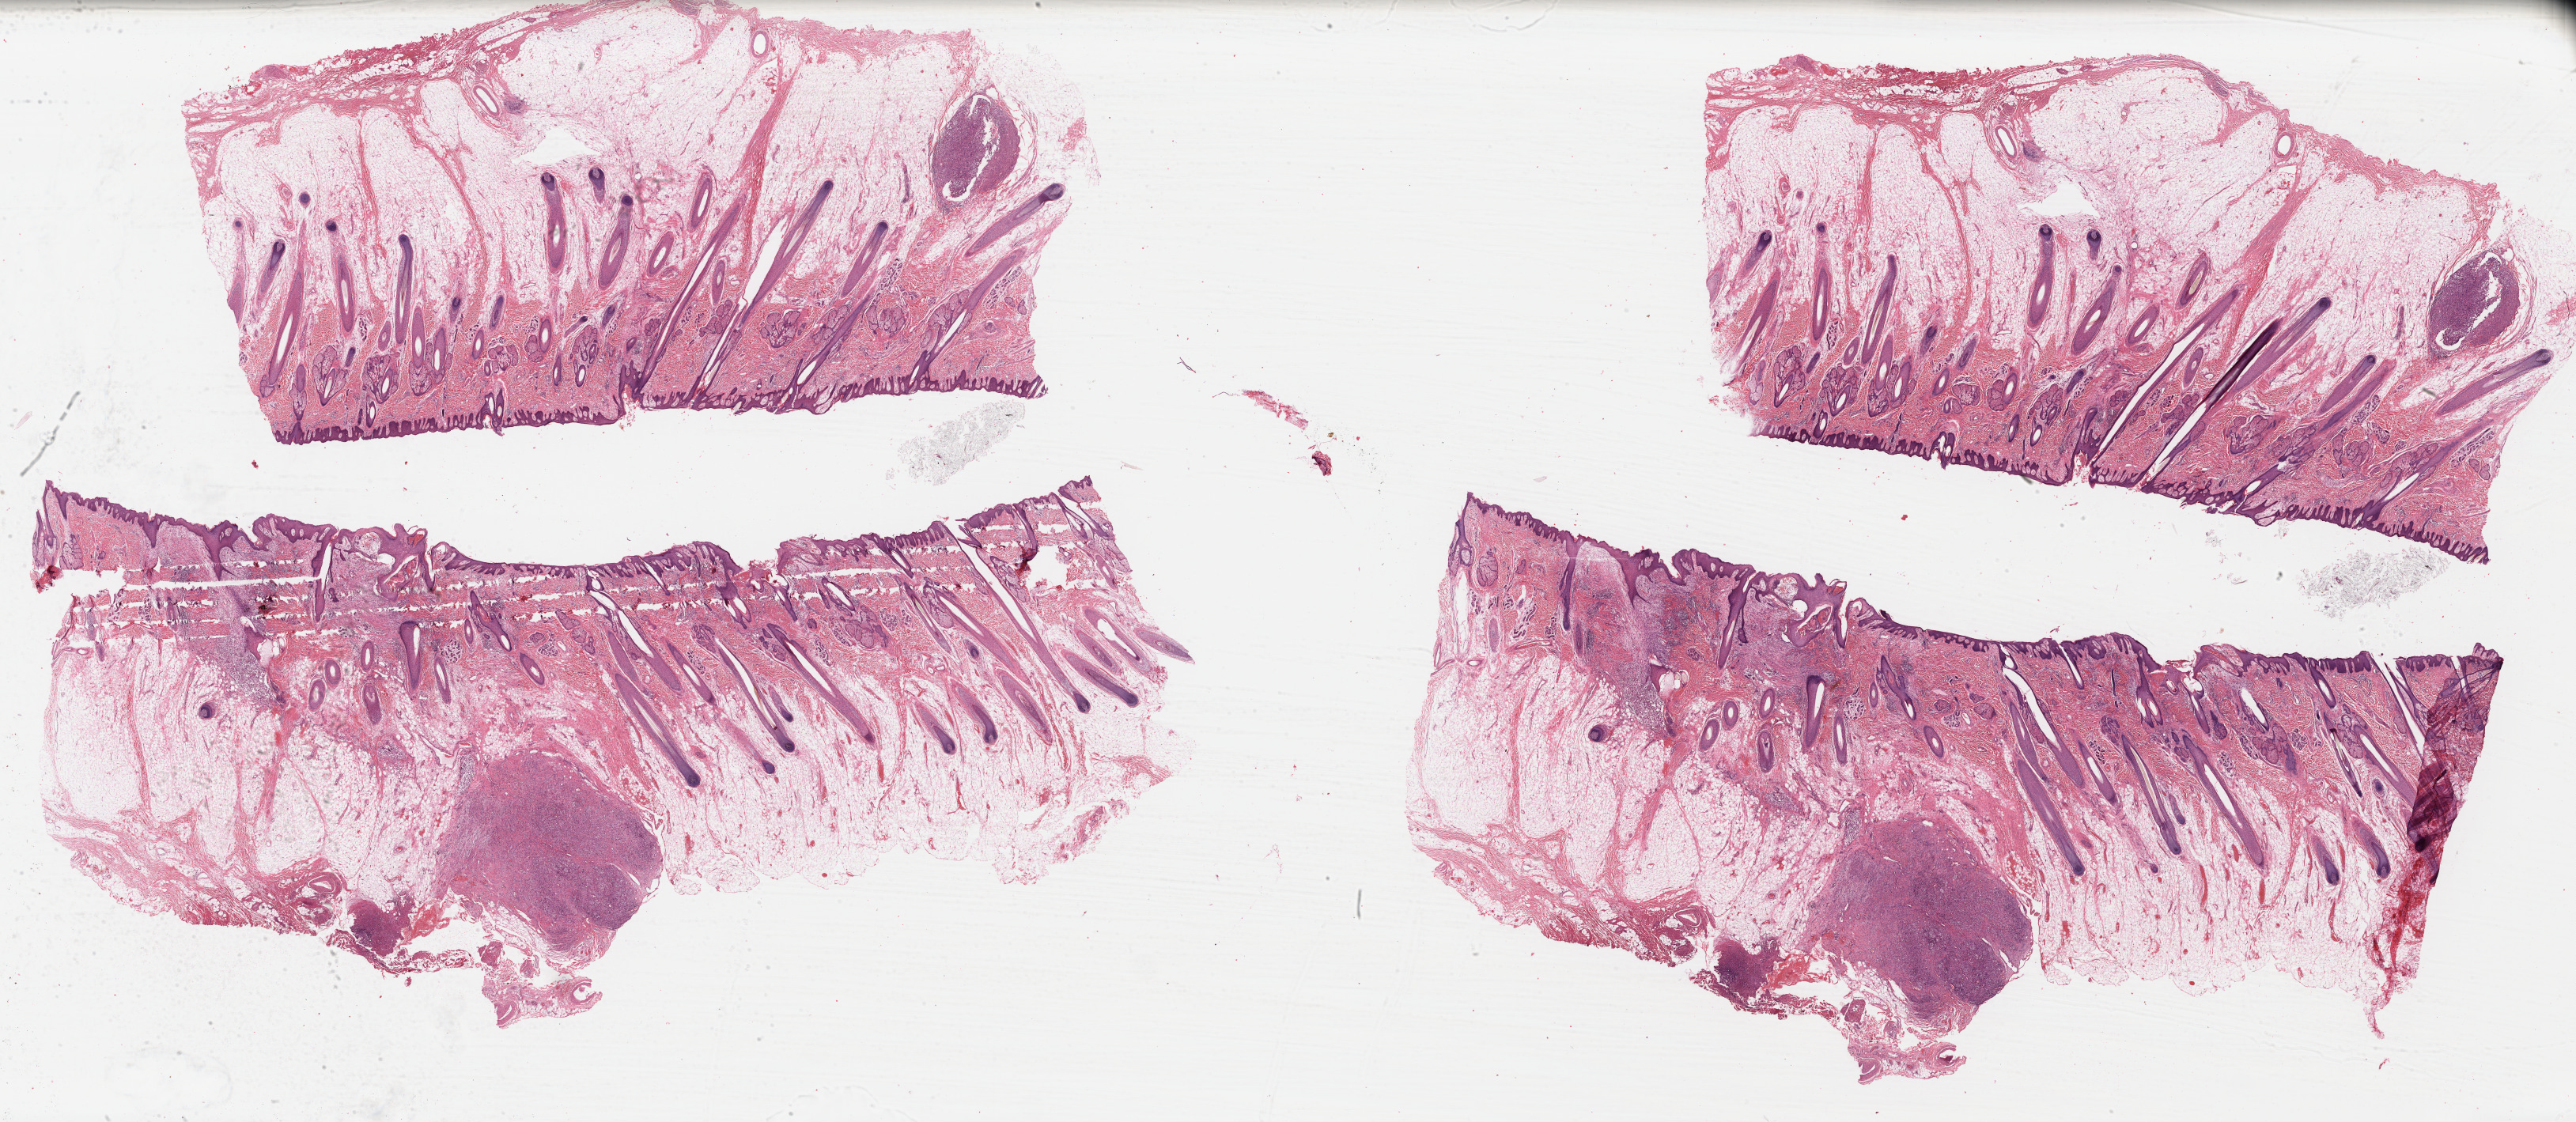
H&E whole-slide image, a low-resolution overview of the entire scanned area, about 51.2 x 22.3 mm (slide scanned at 40x); formalin-fixed paraffin-embedded (FFPE) diagnostic section; metastatic tumour sample. Patient: male, age at initial diagnosis 19 years.
This section: metastatic tumour tissue. Patient diagnosis: Malignant melanoma, NOS.